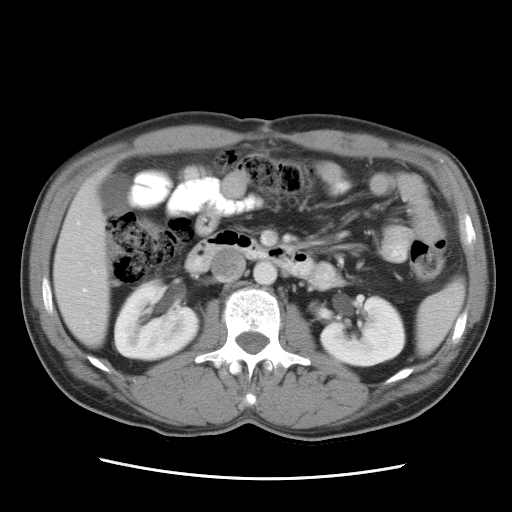
Contrast-enhanced abdominal CT, one axial slice. Position 11 of 34 along the scan axis. 120 kVp. Intravenous contrast given. Soft-tissue window (W 400 / L 40 HU). 7.5 mm slice thickness. 512 × 512 image matrix, field of view 360 × 360 mm. Male patient, age 40 years. From the clinical record (not read from this slice): diagnosis: colorectal cancer liver metastases, imaged before liver resection; multiple liver metastases: yes.
Annotated regions visible in this slice (expert manual segmentation):
- liver: box from (x=54, y=175) to (x=110, y=346) px
- planned liver remnant (the part of the liver to remain after resection): (x=54, y=175)–(x=110, y=346)
- portal vein (with intrahepatic branches): (x=83, y=271)–(x=95, y=292)